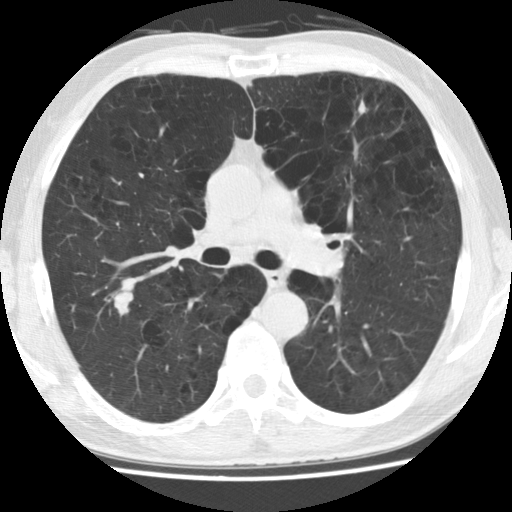
Chest CT (low-dose screening protocol), one axial image, baseline annual screen, lung window (W 1500 / L -600 HU), slice 67 of 158 in the series. Male, age 62 years at enrolment. Current smoker at enrolment.
• Expert-annotated lung lesion, bounding box (x1, y1, x2, y2) in pixels: (92, 264, 149, 326).
• The screening reader recorded 2 non-calcified nodules or masses ≥4 mm on this exam (left upper lobe, right upper lobe); which of them this box marks is not recorded.
• Official screen result: positive, change unspecified: nodule(s) >= 4 mm or enlarging nodule(s), mass(es), or other non-specific abnormalities suspicious for lung cancer.